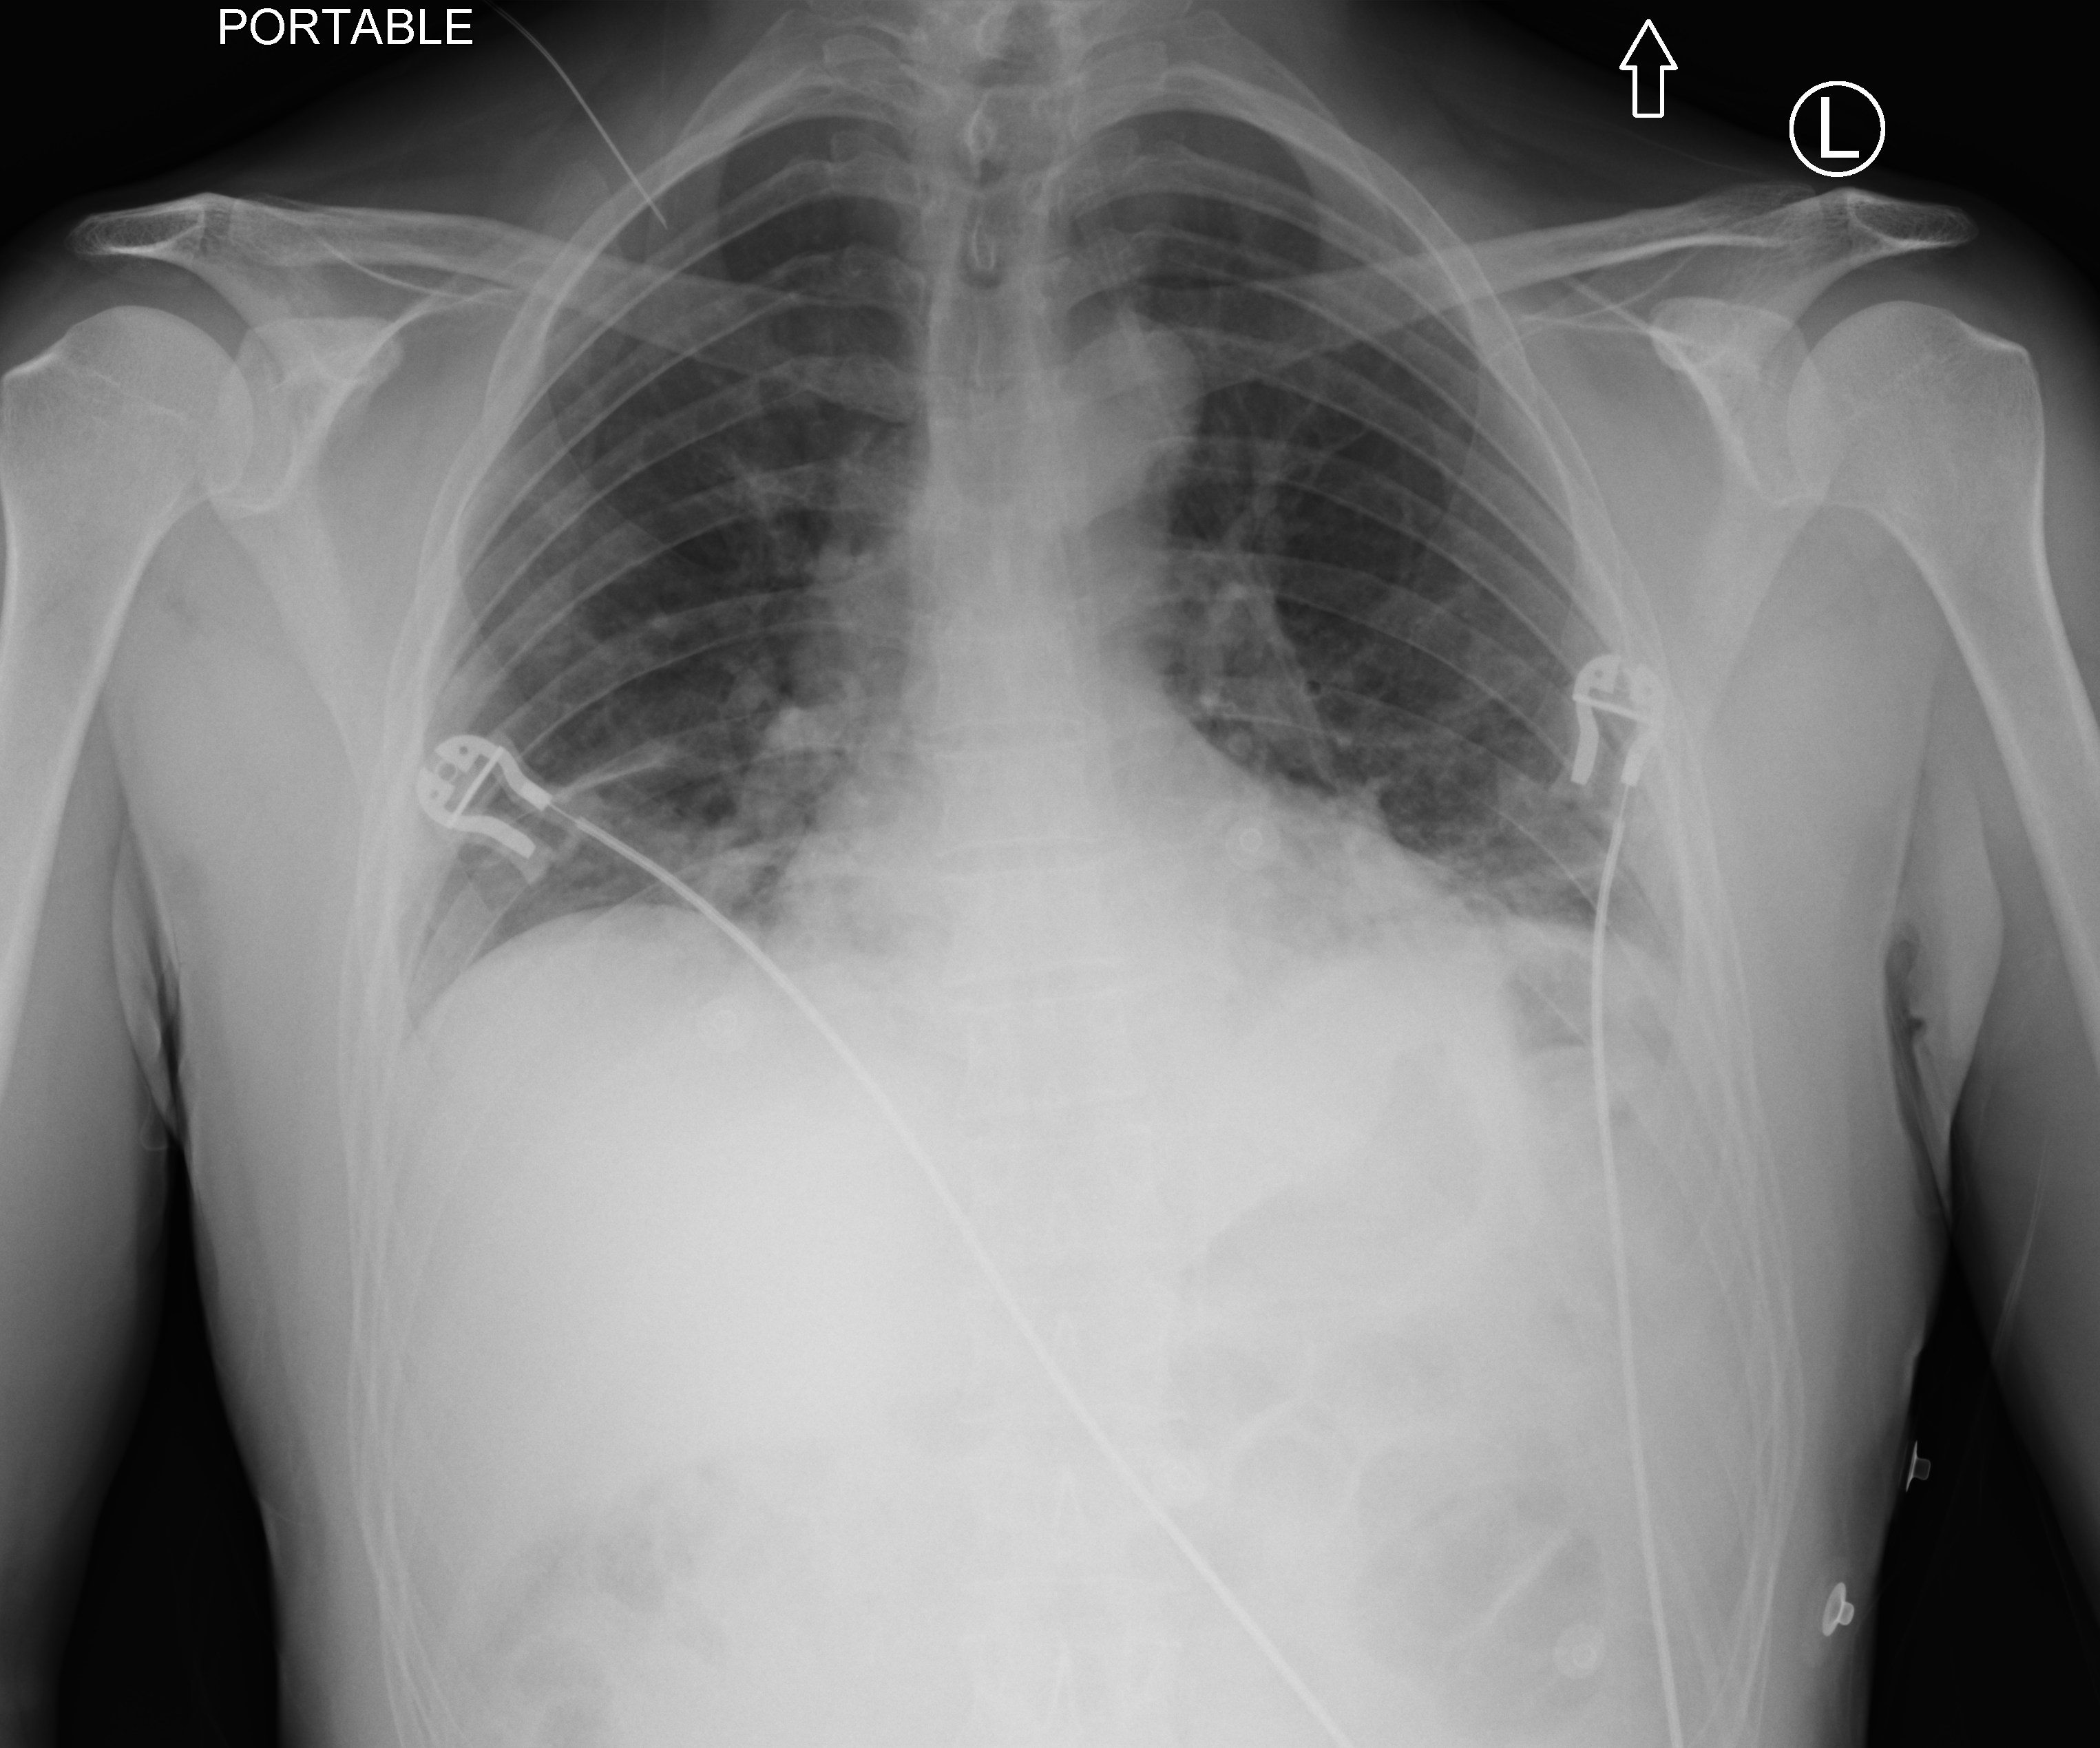
Bedside chest radiograph (computed radiography), anteroposterior (AP) projection. Patient hospitalised with COVID-19; male, aged 18–59 years.
Hospital-stay facts (about this admission, not read from this image; timing relative to this image not recorded): length of hospital stay: 18 days.